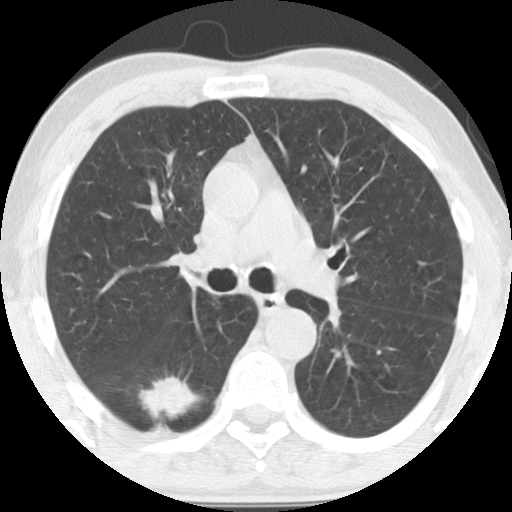
Low-dose screening chest CT, one axial slice. Slice 89 of 135 in the series (ordered by position). Reconstruction kernel STANDARD. 120 kVp. Lung window (W 1500 / L -600 HU). 512 × 512 image matrix, field of view 300 × 300 mm.
Outlined on this slice (outlined manually by an expert reader):
- lesion 1 (tumor, lower lobe of right lung): bounding box (x1, y1, x2, y2) in pixels: (139, 377, 195, 417)